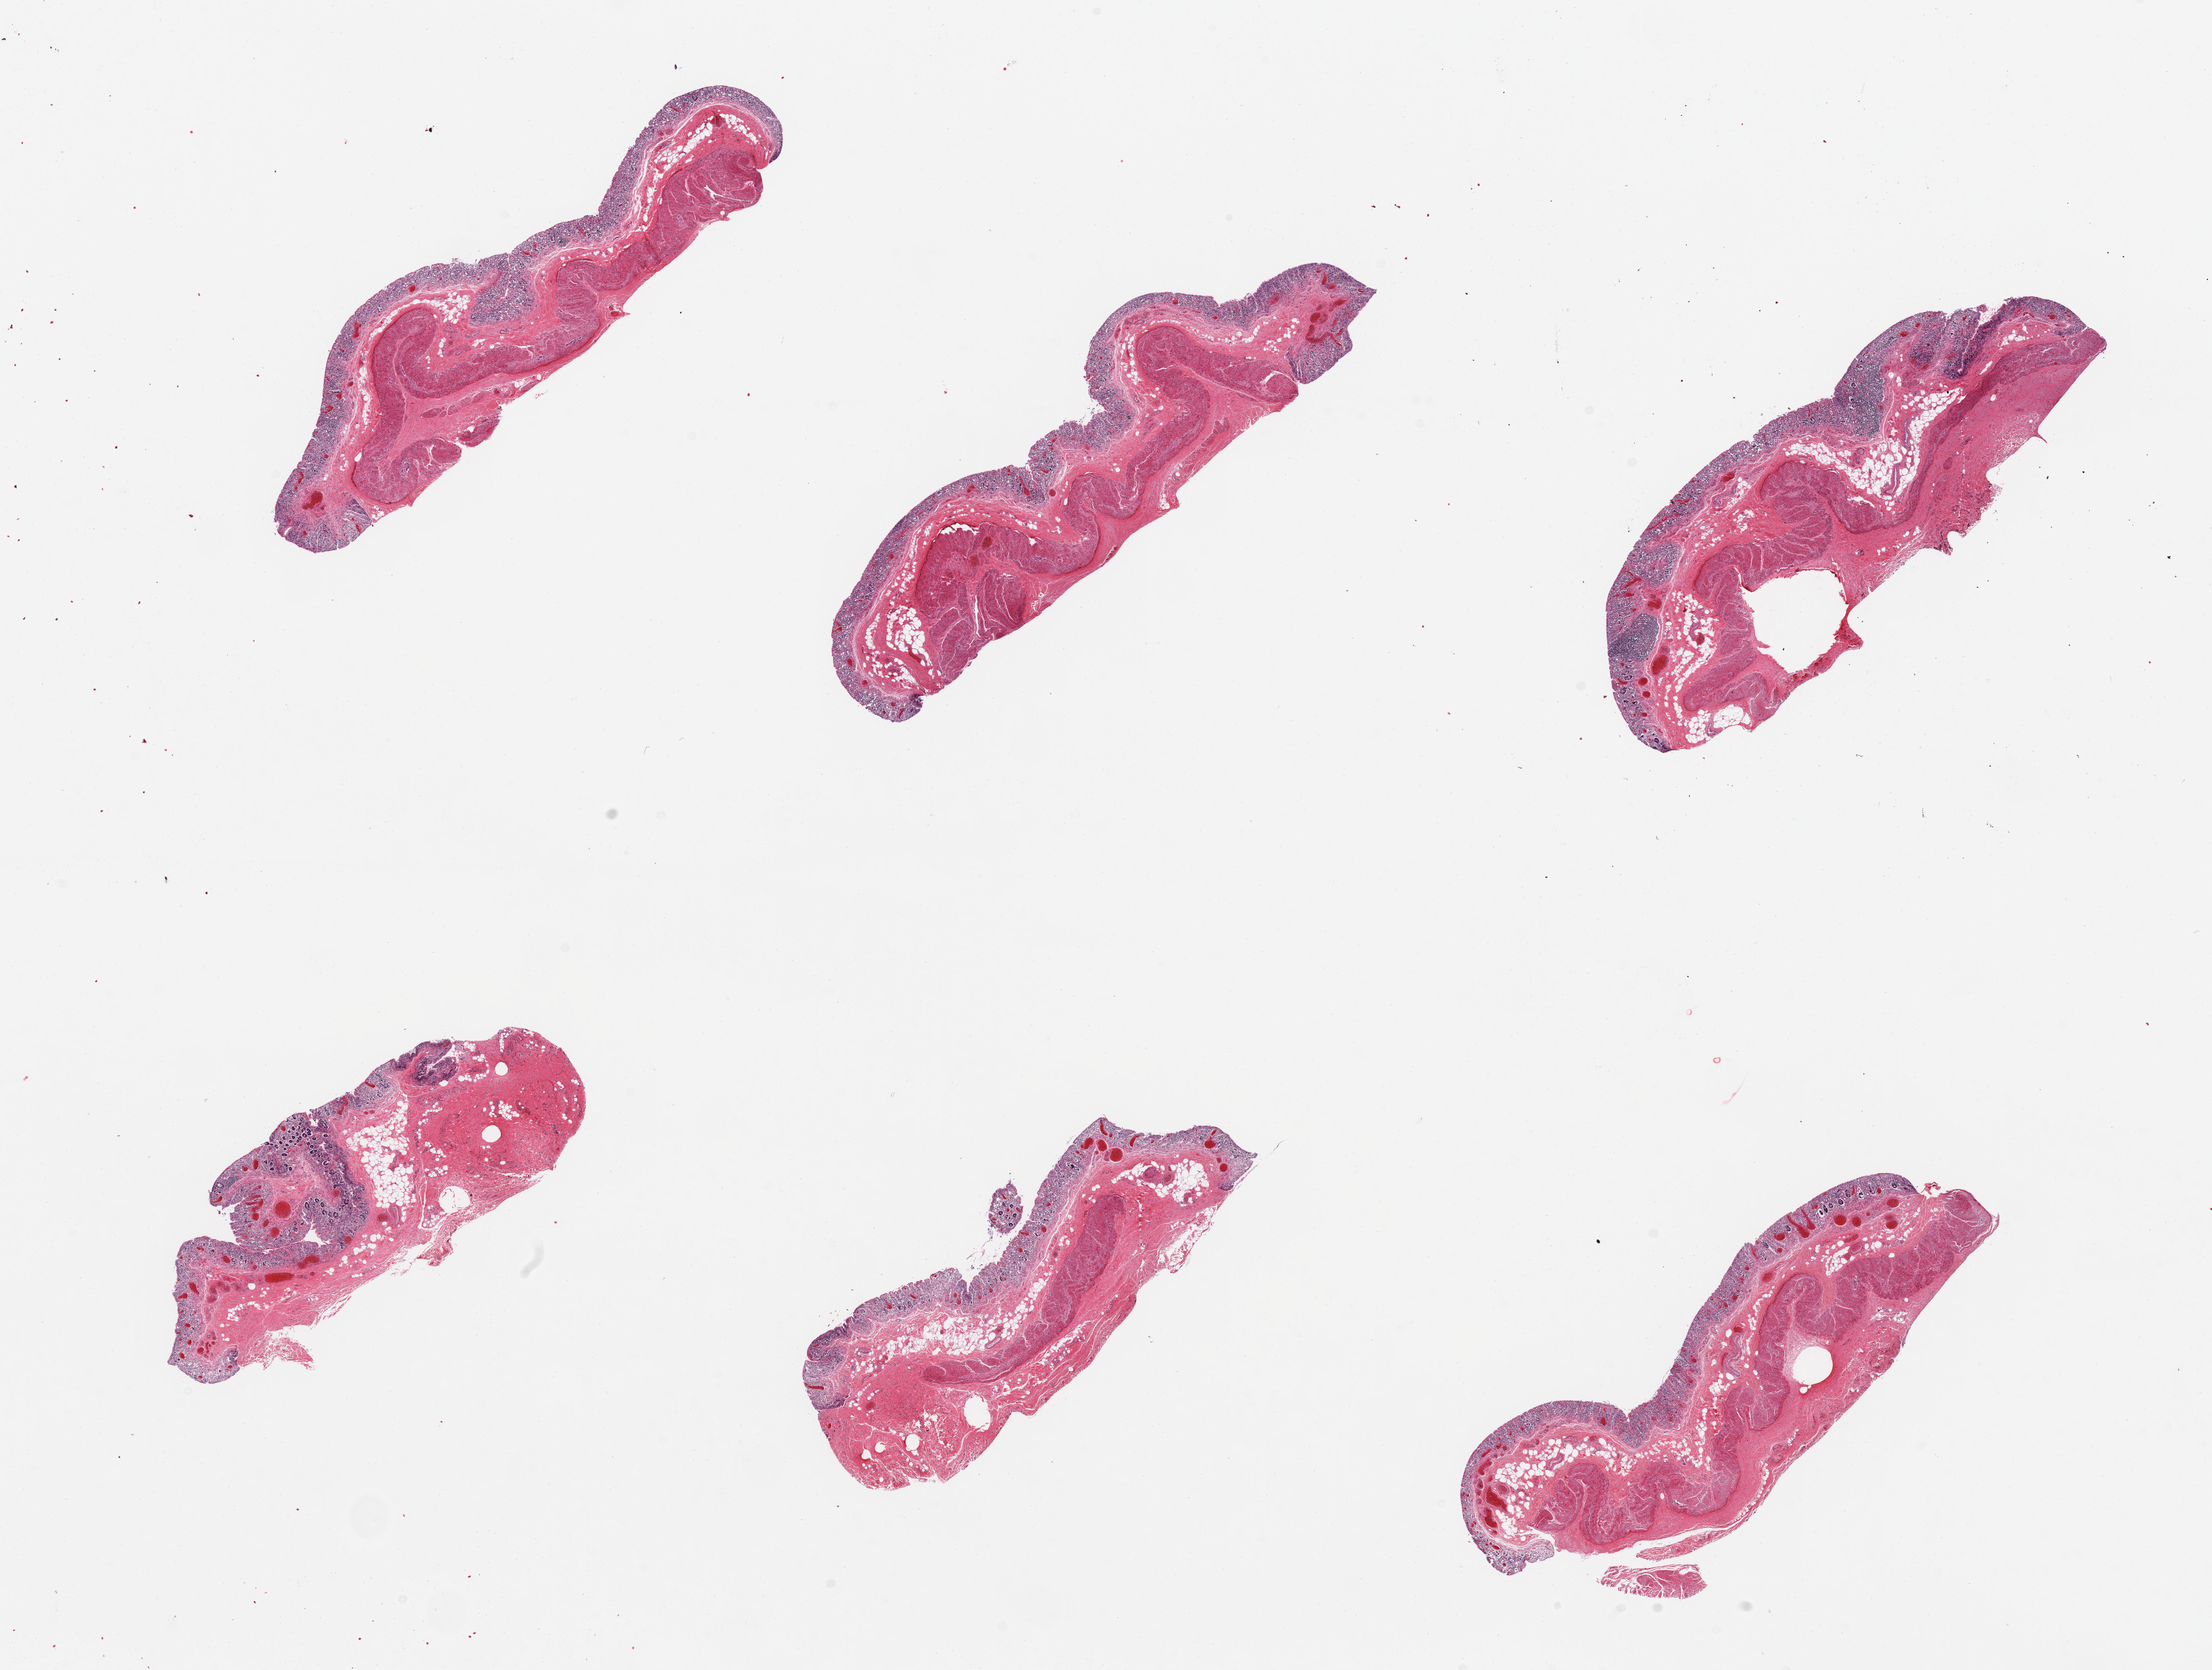
Haematoxylin and eosin whole-slide image, a low-resolution overview of the entire scanned area, about 26.6 x 20.1 mm (acquisition: 20x scan); PAXgene-fixed paraffin-embedded (PFPE) section; target tissue: ileum; tissue donor sample. Donor sex: female.
Review note (as recorded): 6 pieces, mucosa autolyzed, lymphoid aggregates ~5-10% total.